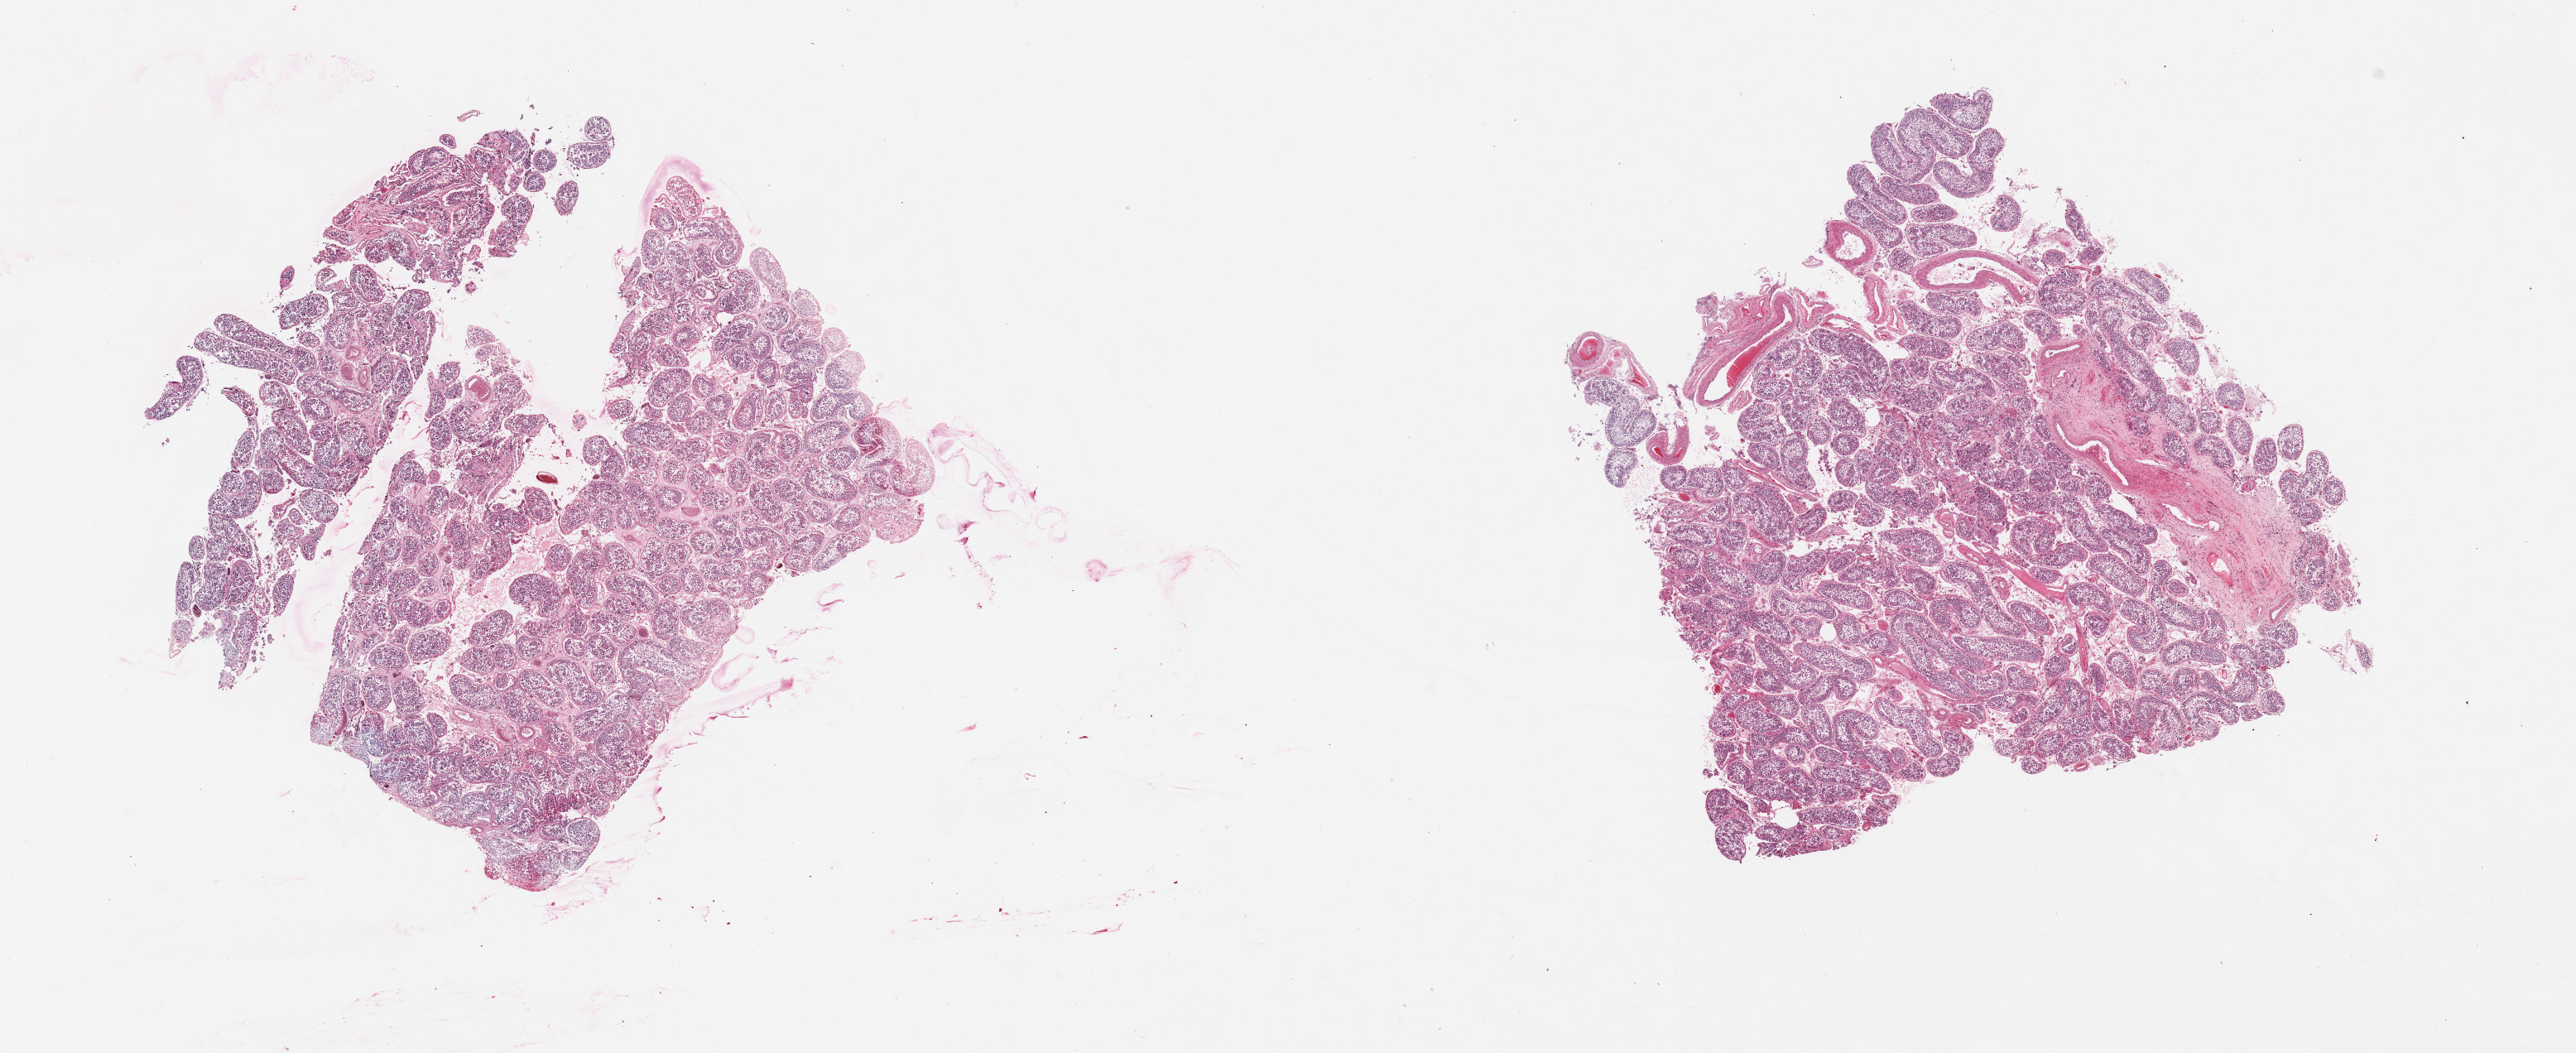
Whole-slide image, haematoxylin and eosin stain, brightfield — shown as a low-resolution overview of the whole scanned area (about 24.6 x 10.1 mm, acquisition: 20x scan), PAXgene-fixed paraffin-embedded (PFPE) section, sampled site (target tissue): testis, donor tissue sample. Donor: male.
• reviewer comment on this tissue sample: 2 pieces; spermatogenesis is present